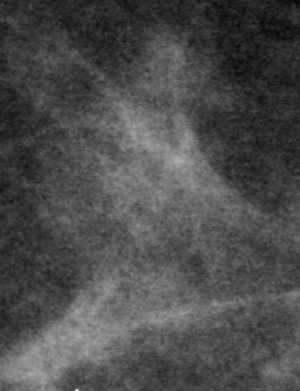
Crop from a digitized film mammogram around one marked abnormality; left breast; MLO view.
Mass, shape irregular, margins ill defined; BI-RADS assessment category 2; subtlety rating 3 on a 1 (subtle) to 5 (obvious) scale; pathology result (as recorded, not read from the image): benign.